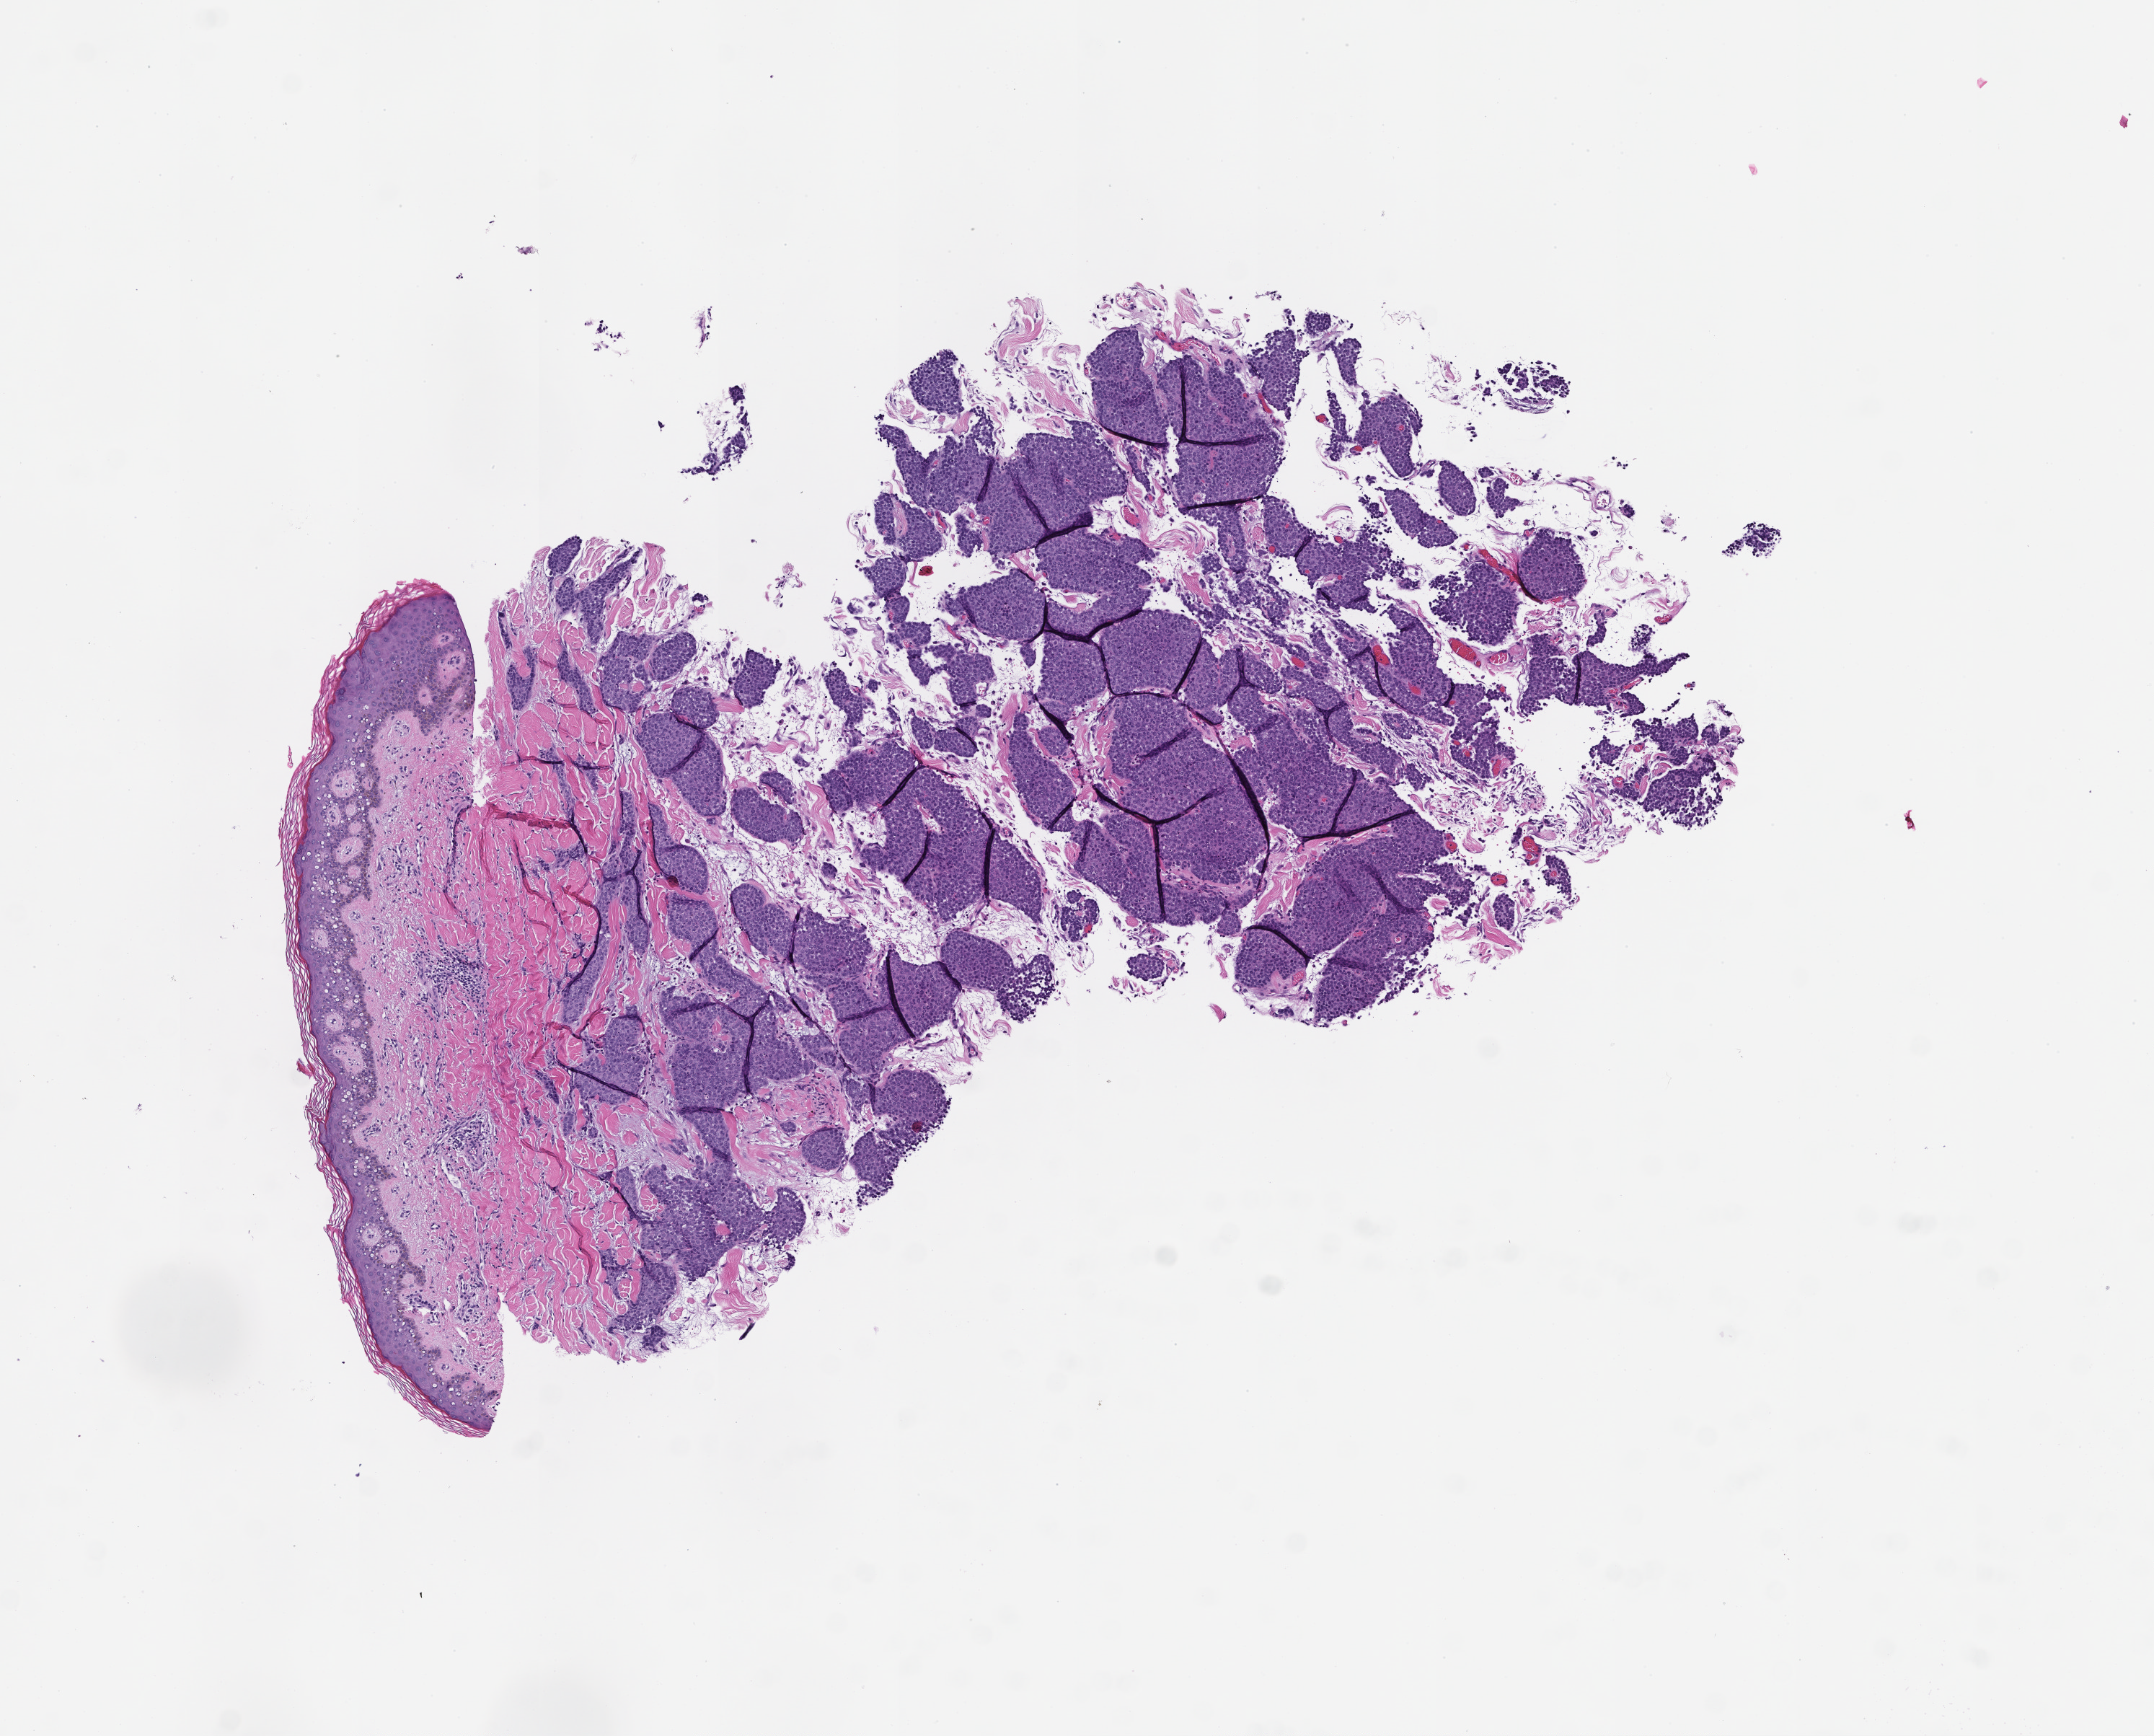
H&E whole-slide image — whole scanned area (about 6.0 x 4.9 mm) shown as a low-resolution overview; FFPE section; collected at baseline (before treatment). Patient: male.
* this section: metastasis (sampled organ not recorded)
* primary diagnosis of the patient: Non-Small Cell Lung Carcinoma